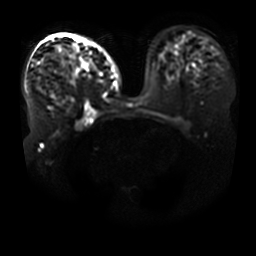
Breast MRI, one axial slice; slice 22 of 41 in the series (ordered by position); diffusion-weighted series; image 2 of 4 stored at this slice position (different b-values; order by instance number); 3 T; 256 × 256 image matrix, field of view 400 × 400 mm. Female patient.
Annotated regions visible in this slice (manually delineated by an expert):
- tumour on diffusion-weighted imaging: bounding box <55,46,98,72> (left, top, right, bottom; pixels)